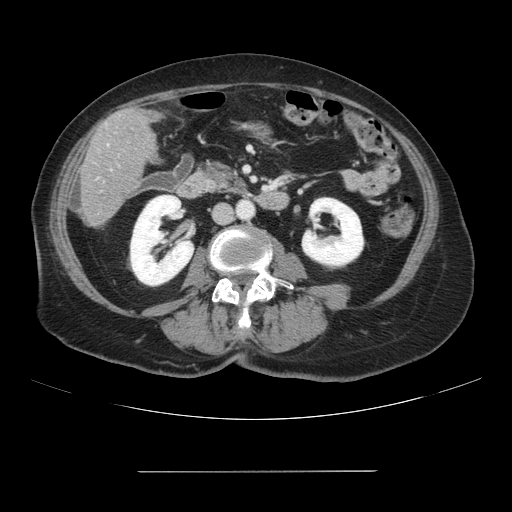
Contrast-enhanced abdominal CT, one axial slice. Position 16 of 111 along the scan axis. 120 kVp. Intravenous contrast given. Soft-tissue window (W 400 / L 40 HU). 2.5 mm slice thickness. 512 × 512 image matrix, field of view 400 × 400 mm. Female patient, age 74 years. Case-level facts recorded for this patient, not image findings: diagnosis: colorectal cancer liver metastases, imaged before liver resection; multiple liver metastases: yes; largest metastasis: 1.1 cm; disease in both lobes: yes.
Structures marked on this image (outlined manually by an expert reader):
- liver: bounding box [x1, y1, x2, y2] px = [81, 107, 157, 228]